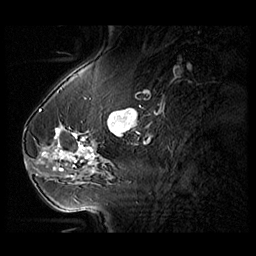
Breast MRI (dynamic contrast-enhanced), one sagittal slice; position 36 of 104 along the scan axis; 3 images stored at this slice position (order not interpretable as contrast timing); 1.5 T; TE 1.3 ms, TR 5.5 ms; 3 mm slice thickness; 256 × 256 image matrix, field of view 220 × 220 mm. Female patient, age 54 years. From the clinical record (not read from this slice): setting: breast cancer imaged before/during neoadjuvant chemotherapy; receptor status: HR-positive, HER2-negative.
Outlined on this slice (semi-automatically segmented with operator editing):
- analysis volume of interest (the breast-tissue region the enhancement analysis was run in; not a lesion): bounding box [x1, y1, x2, y2] px = [28, 127, 104, 182]
- tumour enhancement mask (voxels above the 140 % enhancement threshold inside the analysis volume of interest): [41, 130, 94, 171]